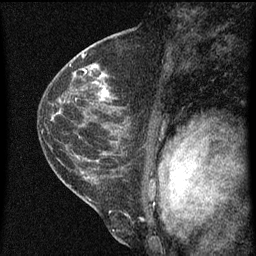
Breast MRI (dynamic contrast-enhanced), one sagittal slice; slice 37 of 60 in the series (ordered by position); dynamic contrast-enhanced series, image 2 of 3 at this slice position (ordered by acquisition); 1.5 T; TE 4.2 ms, TR 8 ms; 2 mm slice thickness; 256 × 256 image matrix, field of view 180 × 180 mm. Female patient, age 48 years.
Annotated regions visible in this slice (semi-automatically segmented with operator editing):
- analysis volume of interest (the breast-tissue region the enhancement analysis was run in; not a lesion): box from (x=82, y=68) to (x=126, y=125) px
- tumour enhancement mask (voxels above the 70 % enhancement threshold inside the analysis volume of interest): (x=85, y=70)–(x=112, y=99)